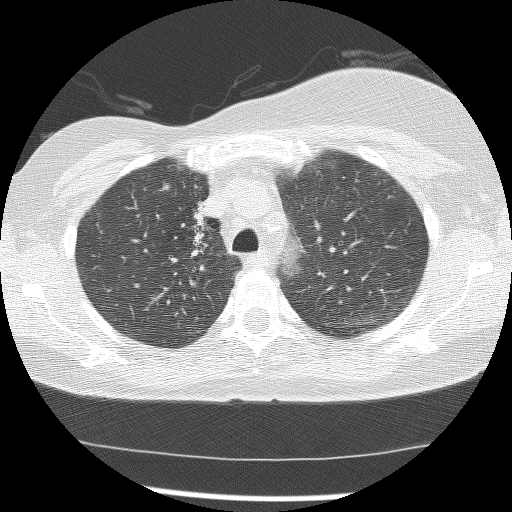
Axial slice from a low-dose chest CT screening exam; baseline annual screen; lung window (W 1500 / L -600 HU); 2.5 mm slice thickness; lung (sharp) reconstruction kernel (BONE); slice 39 of 172 in the series; 512 × 512 image matrix, field of view 315 × 315 mm. Female, age 56 years at enrolment. Current smoker at enrolment.
Expert-annotated lung lesion, bounding box [x1, y1, x2, y2] px = [165, 193, 223, 272]. The screening reader recorded 2 non-calcified nodules or masses ≥4 mm on this exam (right lower lobe, right middle lobe); which of them this box marks is not recorded. Later outcome: lung cancer diagnosed 1185 days after this screen (after the third annual screen) — adenocarcinoma, NOS, right upper lobe, stage IIIB (AJCC 6th edition), 8 mm at pathology.